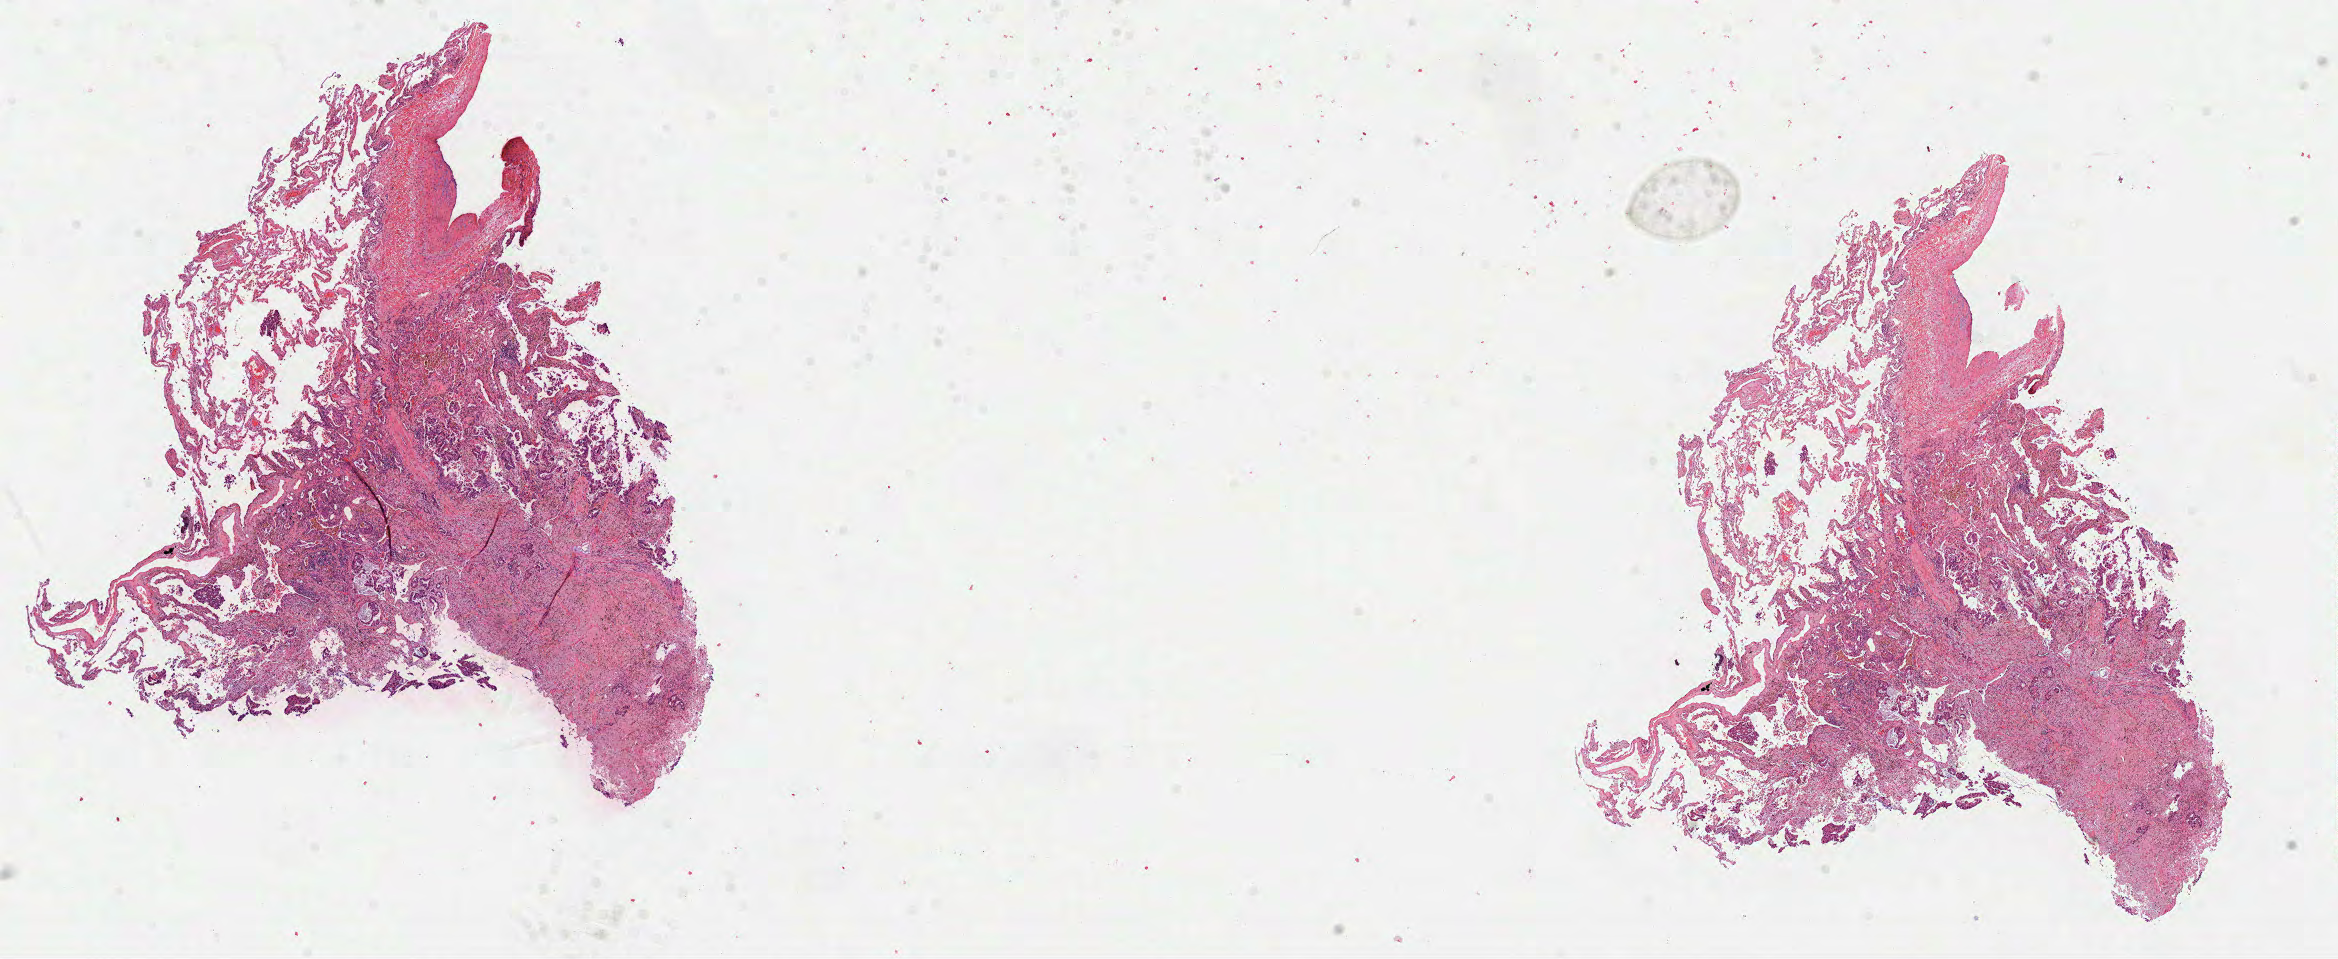
H&E whole-slide image, low-resolution overview of the scanned area, about 18.9 x 7.7 mm (acquisition: 40x scan), FFPE section, primary tumour sample from the lung. Patient: male, age at initial diagnosis 61 years.
AJCC pathologic stage: IA (7th edition). Histologic diagnosis: Adenocarcinoma, NOS (upper lobe, lung). Laterality: right.